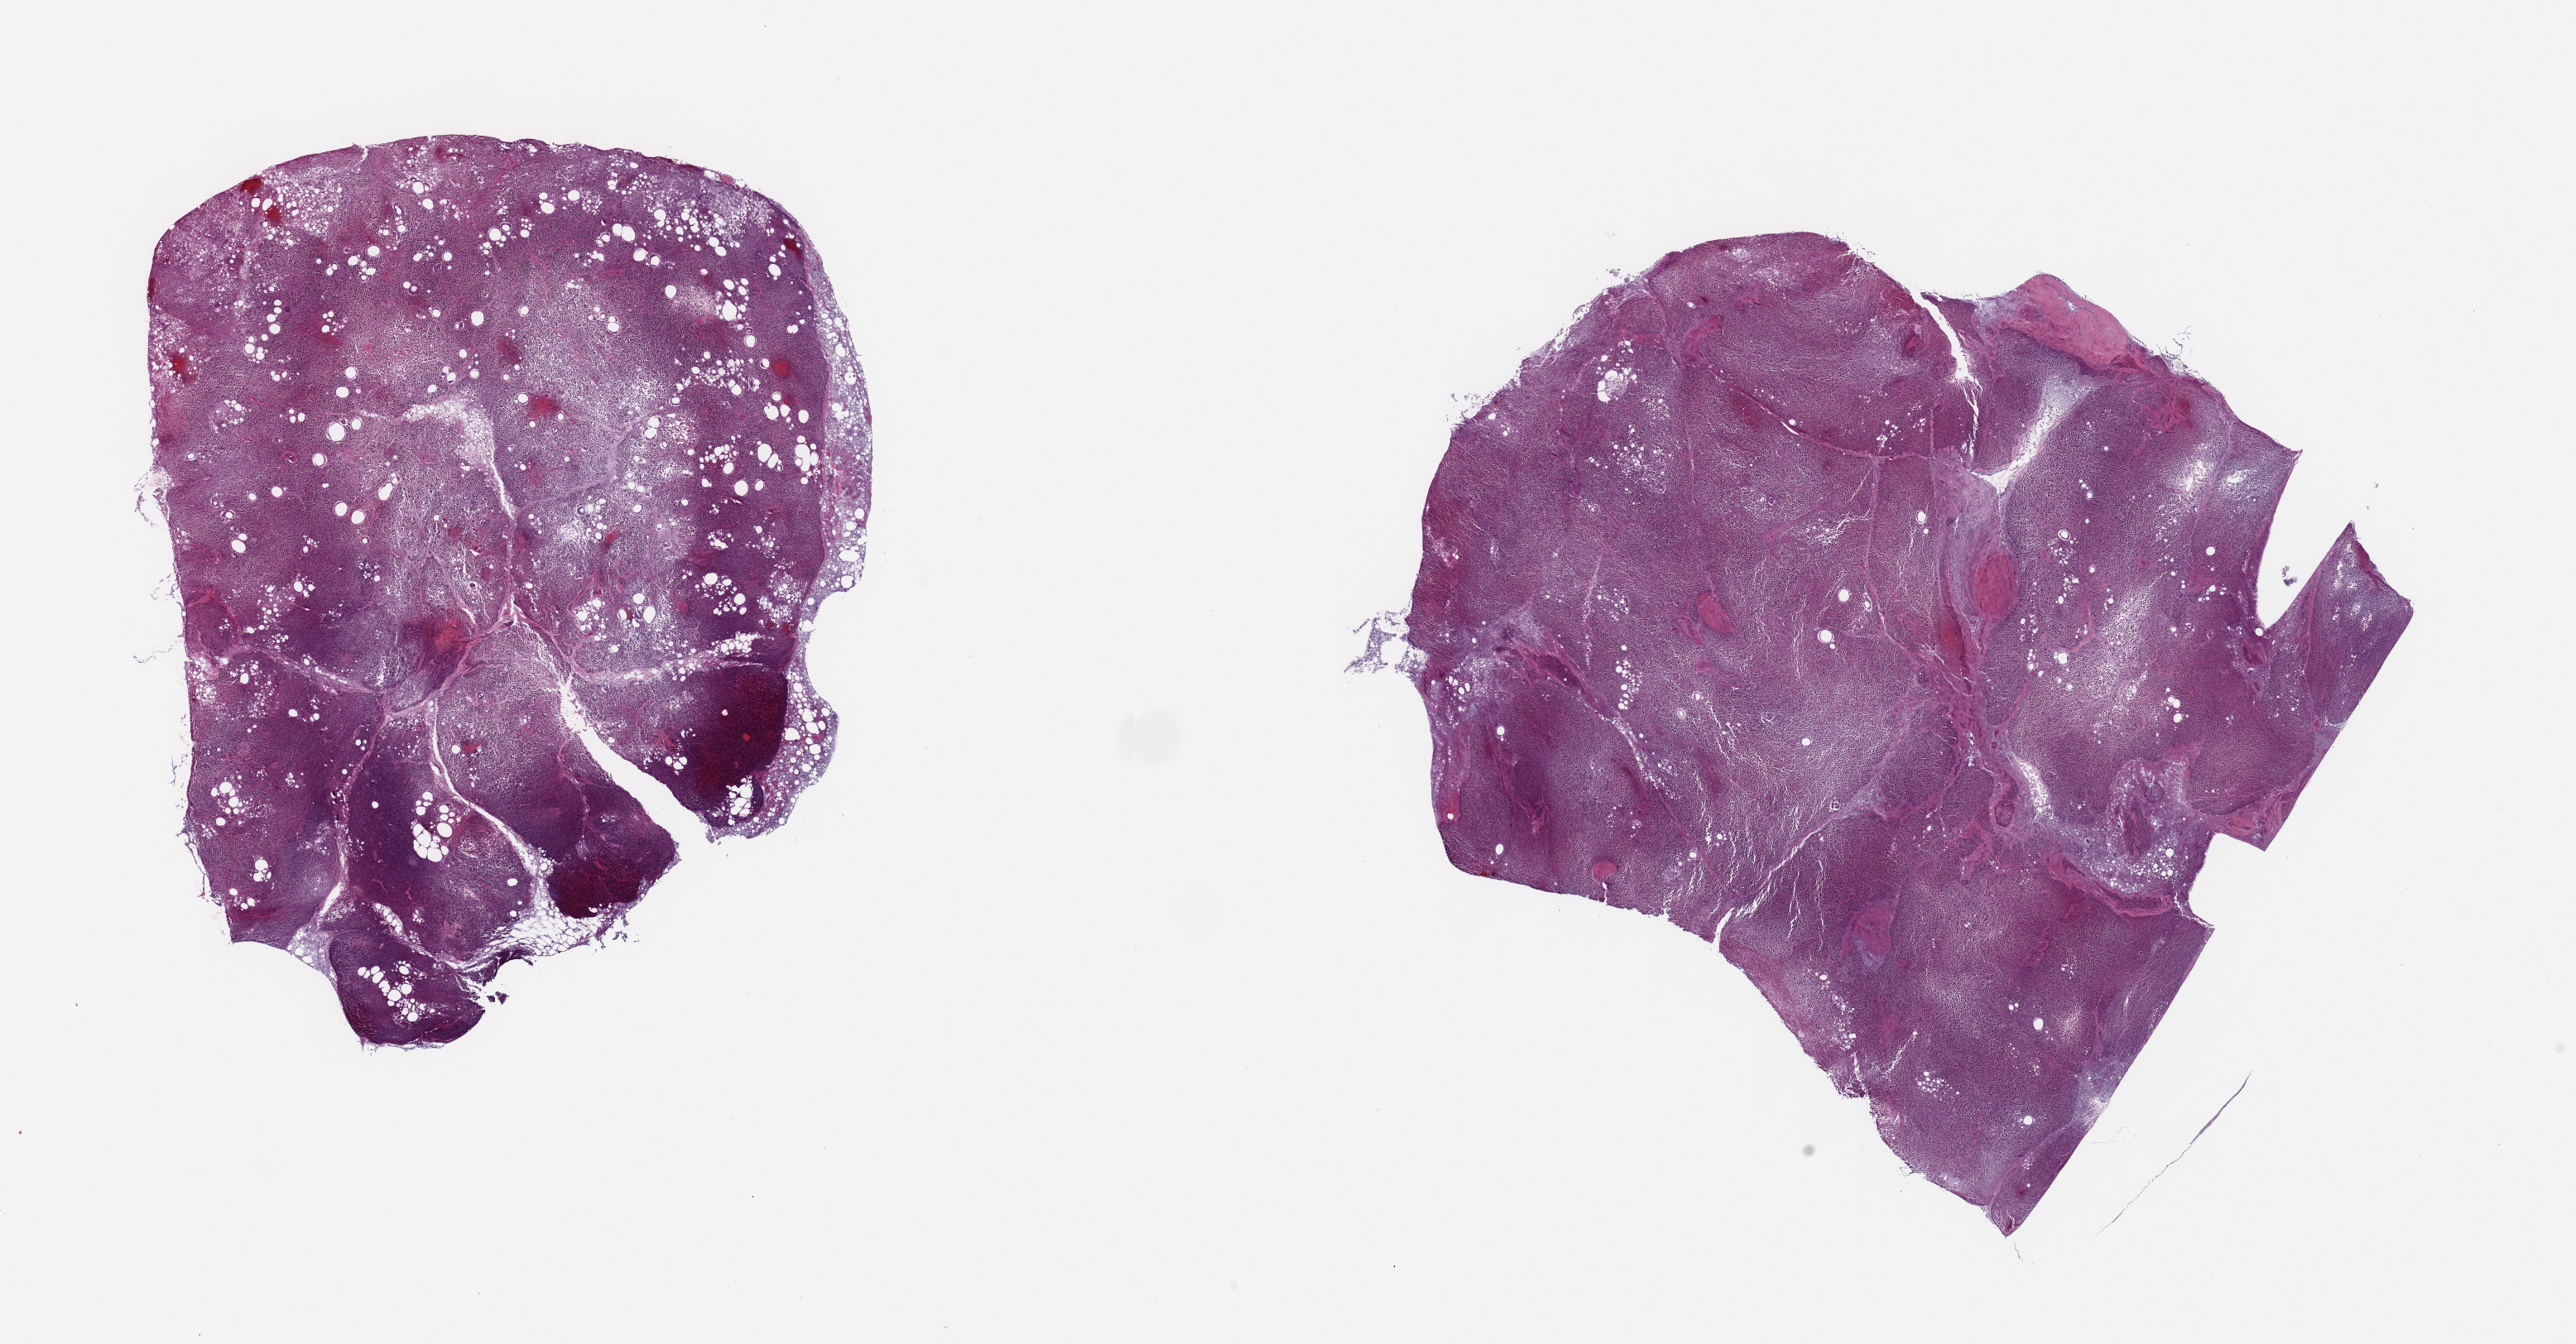
Whole-slide image, H&E stain — low-resolution overview of the scanned area, about 24.6 x 12.8 mm (acquisition: 20x scan), PAXgene-fixed paraffin-embedded (PFPE) section, section of pancreas (target tissue), tissue donor sample. Donor: male.
Pathologist's review note for this sample: 2 pieces; severely autolyzed.